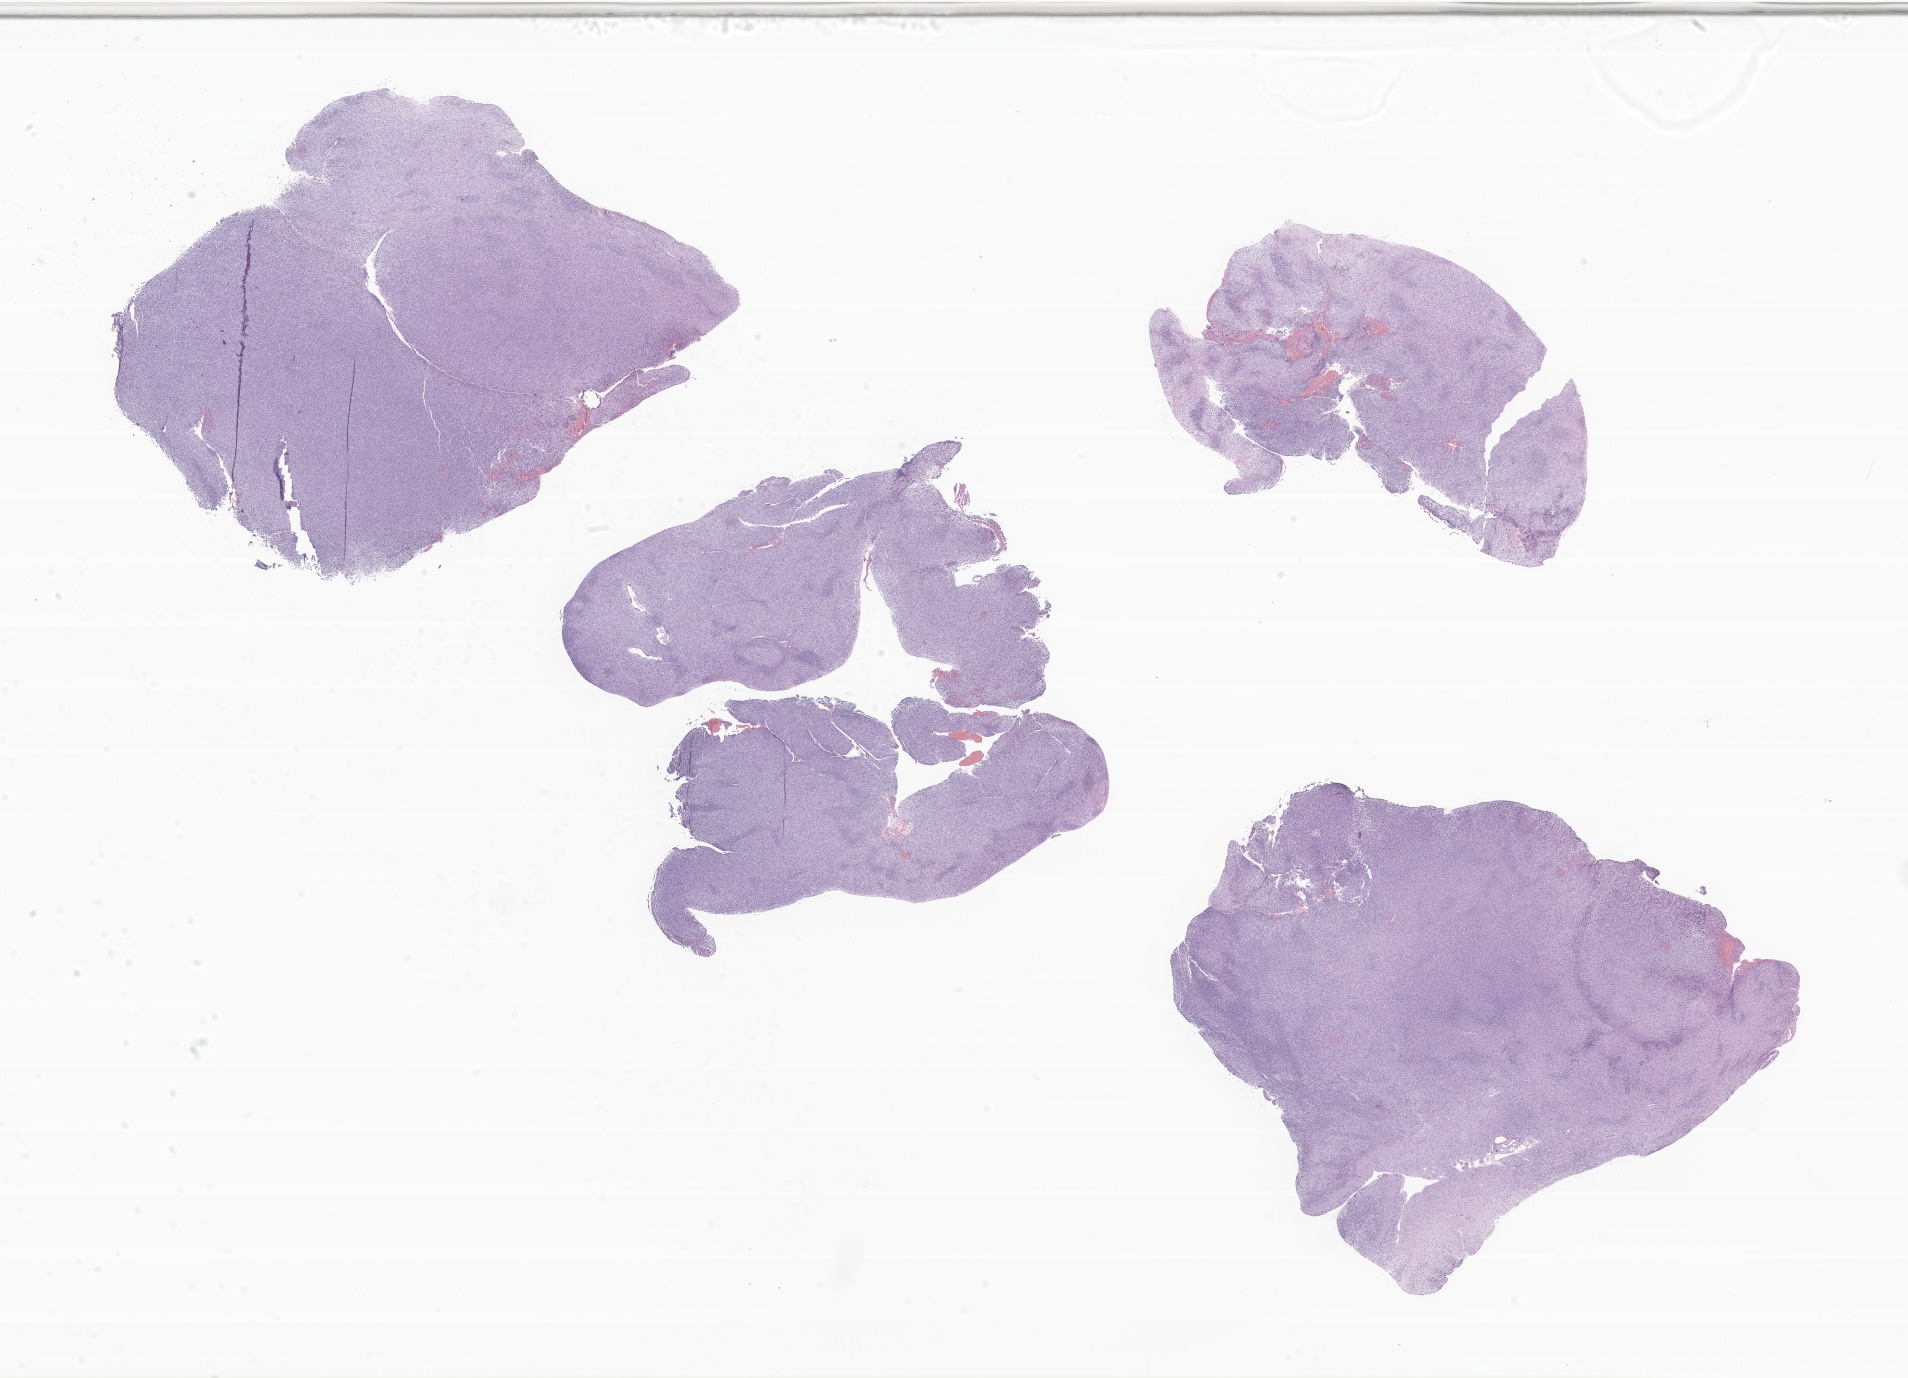
Whole-slide image, H&E stain of tumor tissue from the brain — low-resolution overview of the scanned area, about 32.2 x 23.2 mm; FFPE section. Female patient, age 79 months (6 years 7 months).
• diagnosis (ICD-O-3 morphology term): Medulloblastoma, NOS